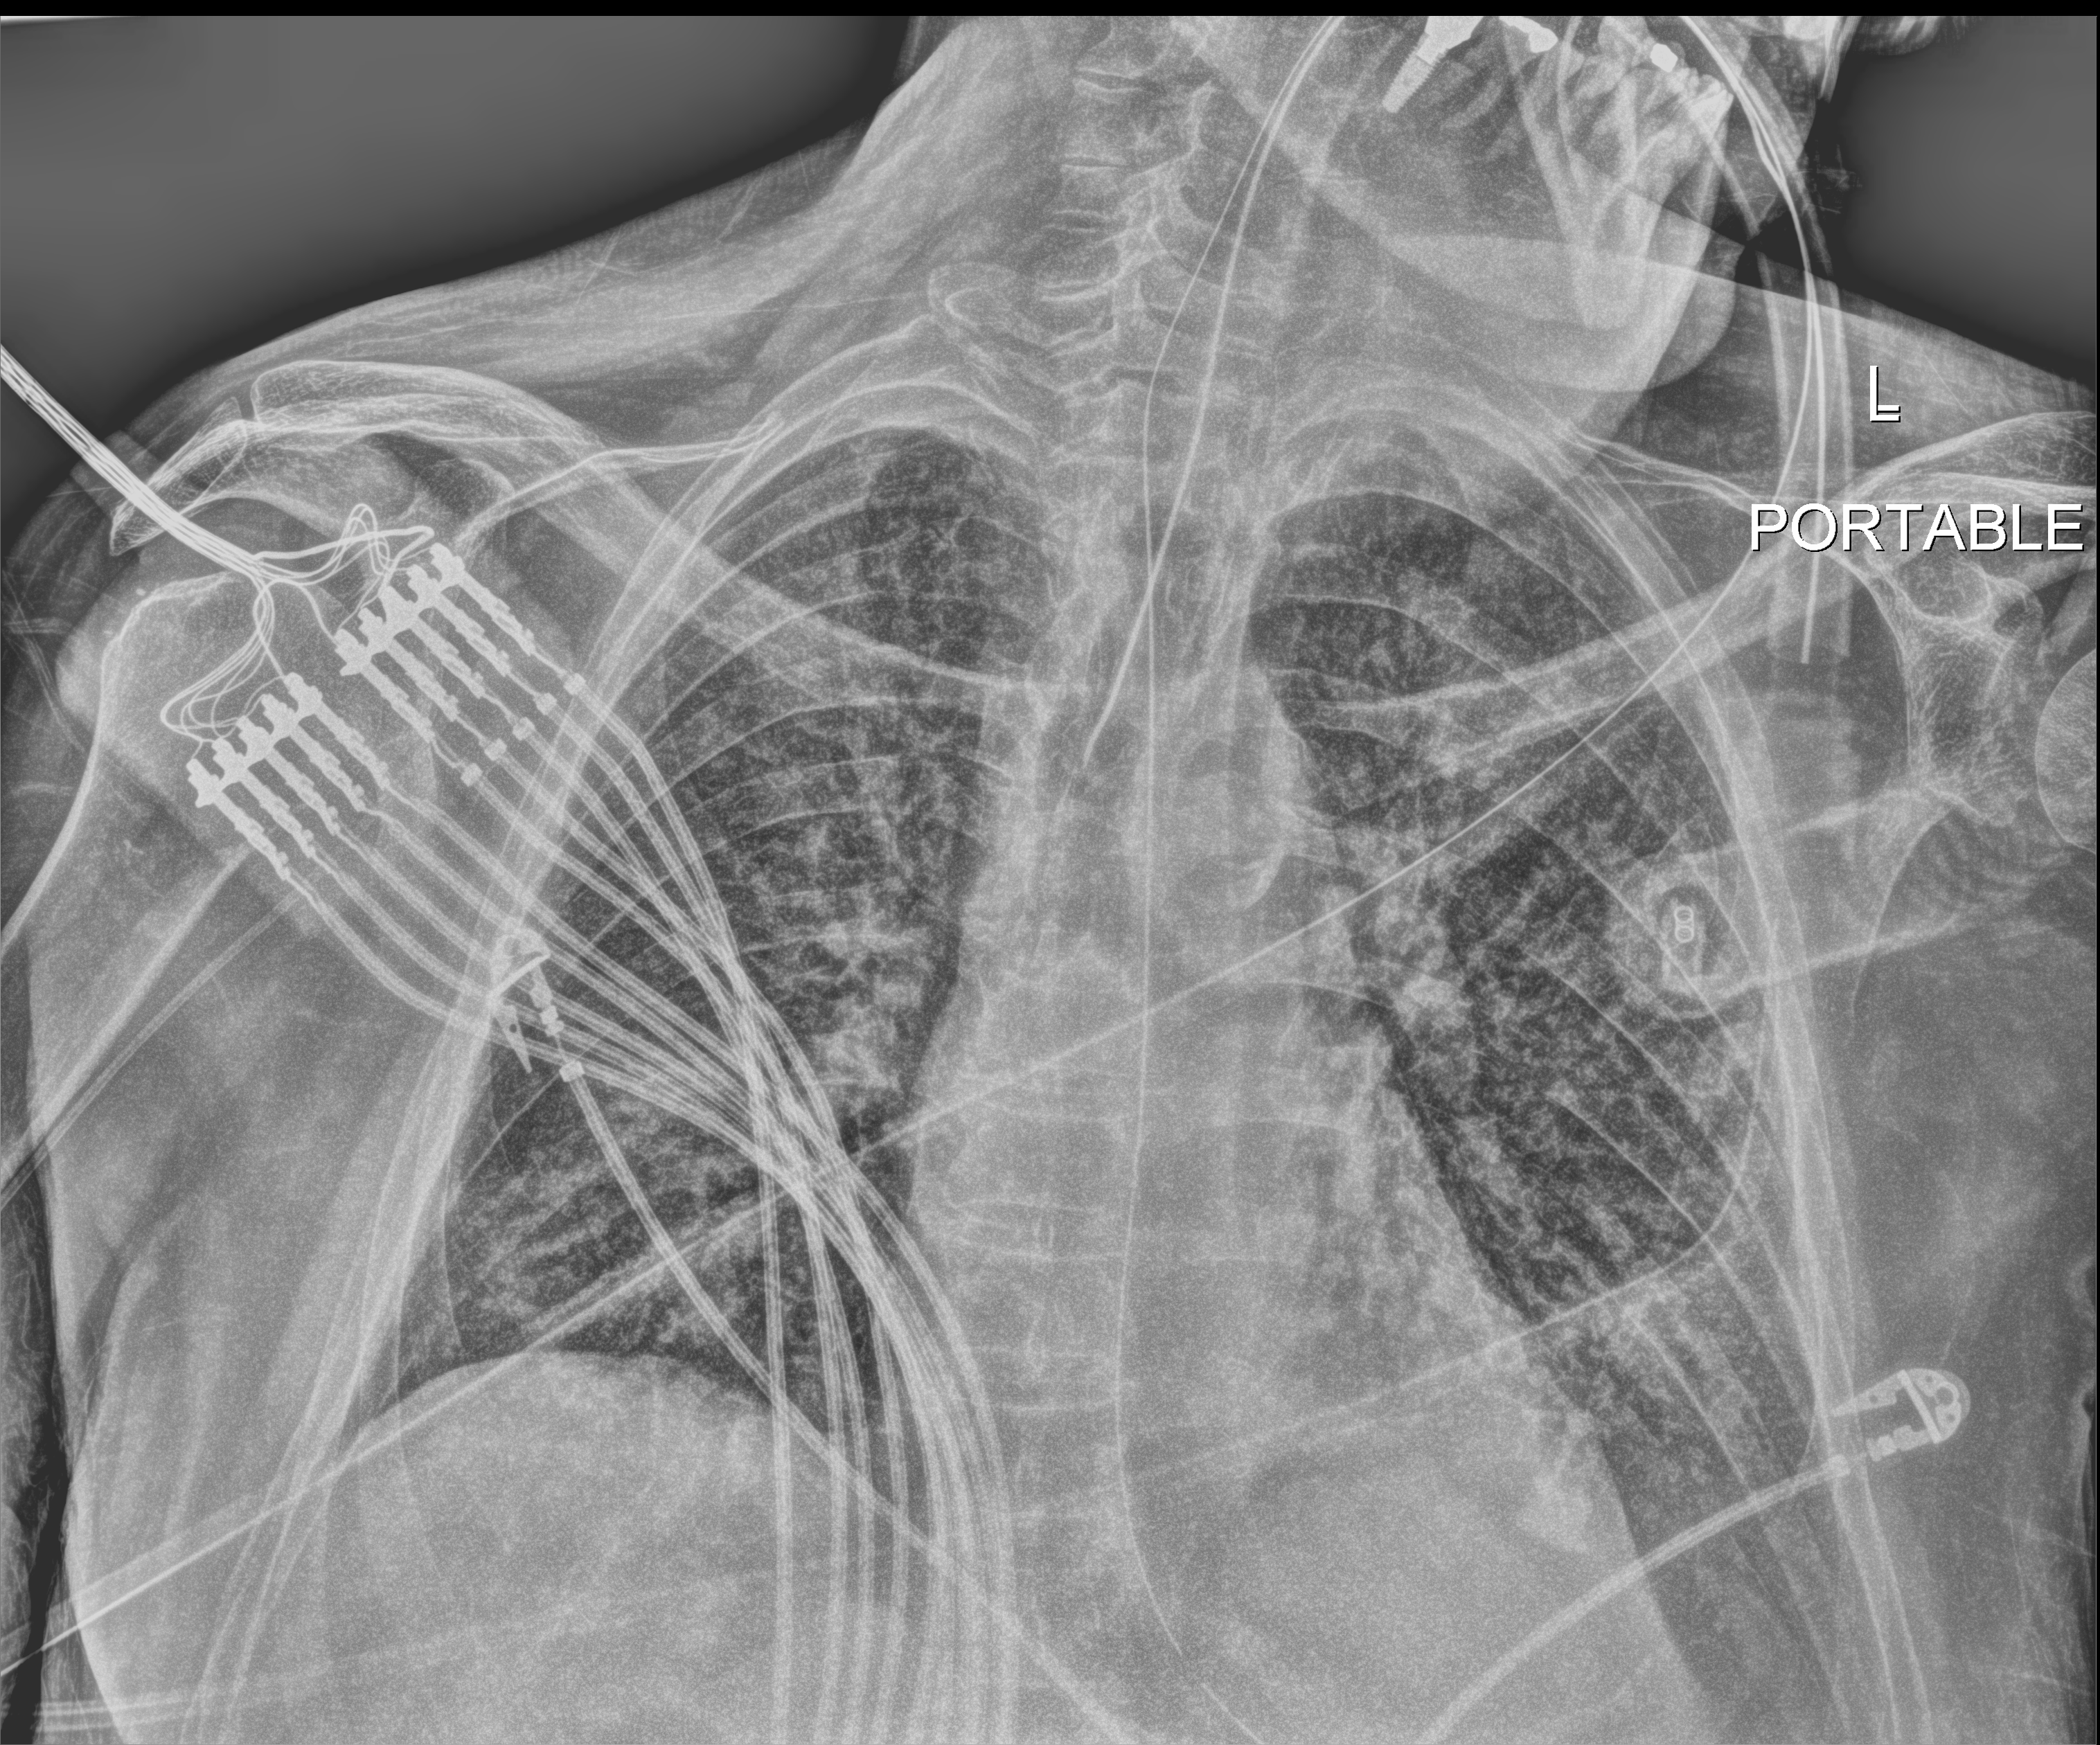
Bedside chest radiograph (digital radiography). Patient hospitalised with COVID-19; male, aged 60–74 years.
Hospital-stay facts (about this admission, not read from this image; timing relative to this image not recorded):
- length of hospital stay: 25 days
- admitted to intensive care during this hospital stay: yes